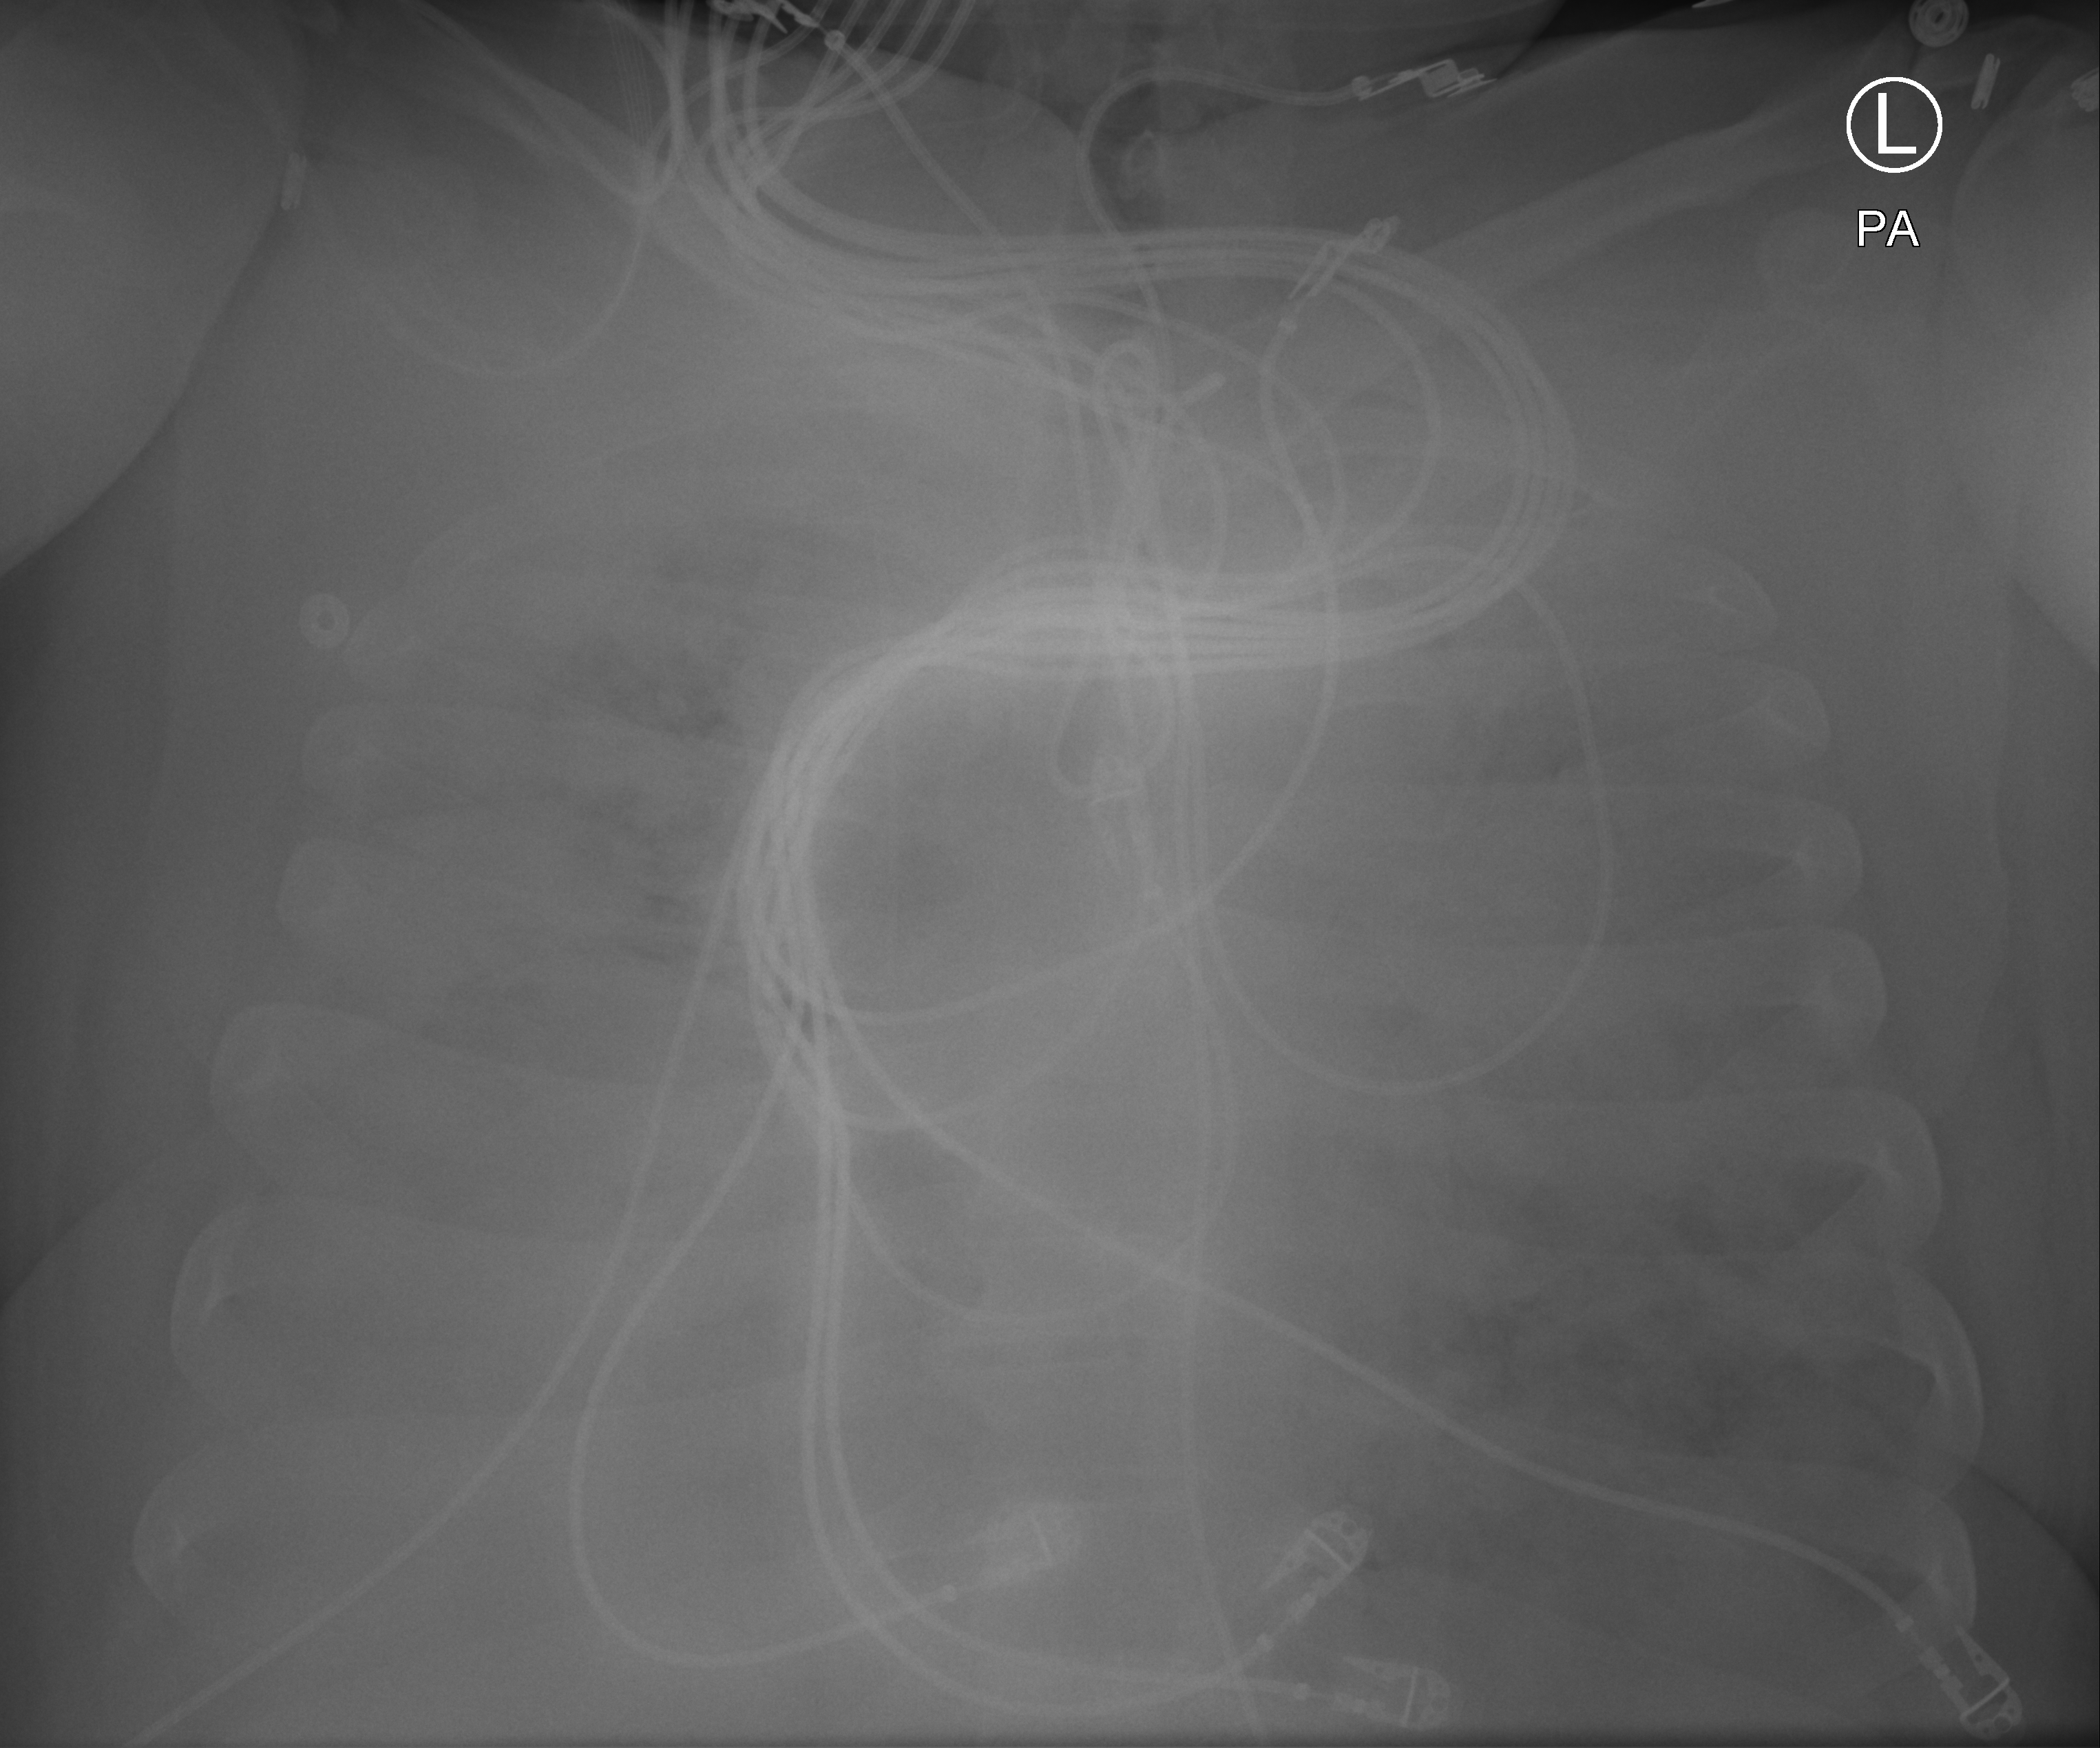
Chest X-ray (portable); posteroanterior (PA) projection. Adult patient hospitalised with COVID-19, age 18–59 years.
Admission-level facts for this patient (not findings on this image; timing relative to this image not recorded): length of hospital stay: 10 days; mechanically ventilated during this hospital stay: yes.